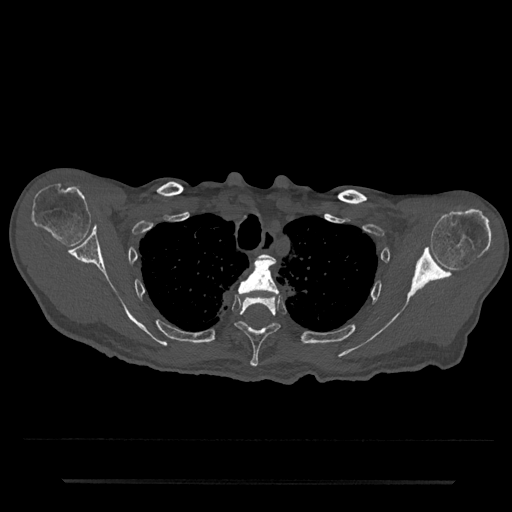
CT including the spine, one axial slice. Position 627 of 797 along the scan axis. Bone window (W 1800 / L 400 HU). 0.5 mm slice thickness. 512 × 512 image matrix, field of view 427 × 427 mm. Patient: male, 74 years. From the clinical record (not read from this slice): primary cancer: prostate.
Structures marked on this image (semi-automatically segmented with operator editing):
- T2 vertebra: bounding box [x1, y1, x2, y2] px = [262, 254, 269, 259]
- T3 vertebra: [237, 256, 279, 296]
- T4 vertebra: [234, 297, 280, 367]